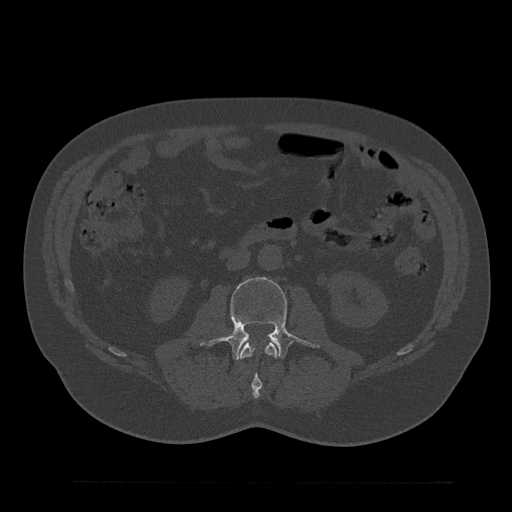
CT including the spine, one axial slice; slice 55 of 797 in the series (ordered by position); 120 kVp; bone window (W 1800 / L 400 HU); 512 × 512 image matrix, field of view 430 × 430 mm. Male patient, age 61 years. Case-level facts recorded for this patient, not image findings: primary cancer: prostate.
Structures marked on this image (semi-automatically segmented with operator editing):
- L2 vertebra: box from (x=239, y=342) to (x=278, y=399) px
- L3 vertebra: (x=205, y=277)–(x=319, y=360)